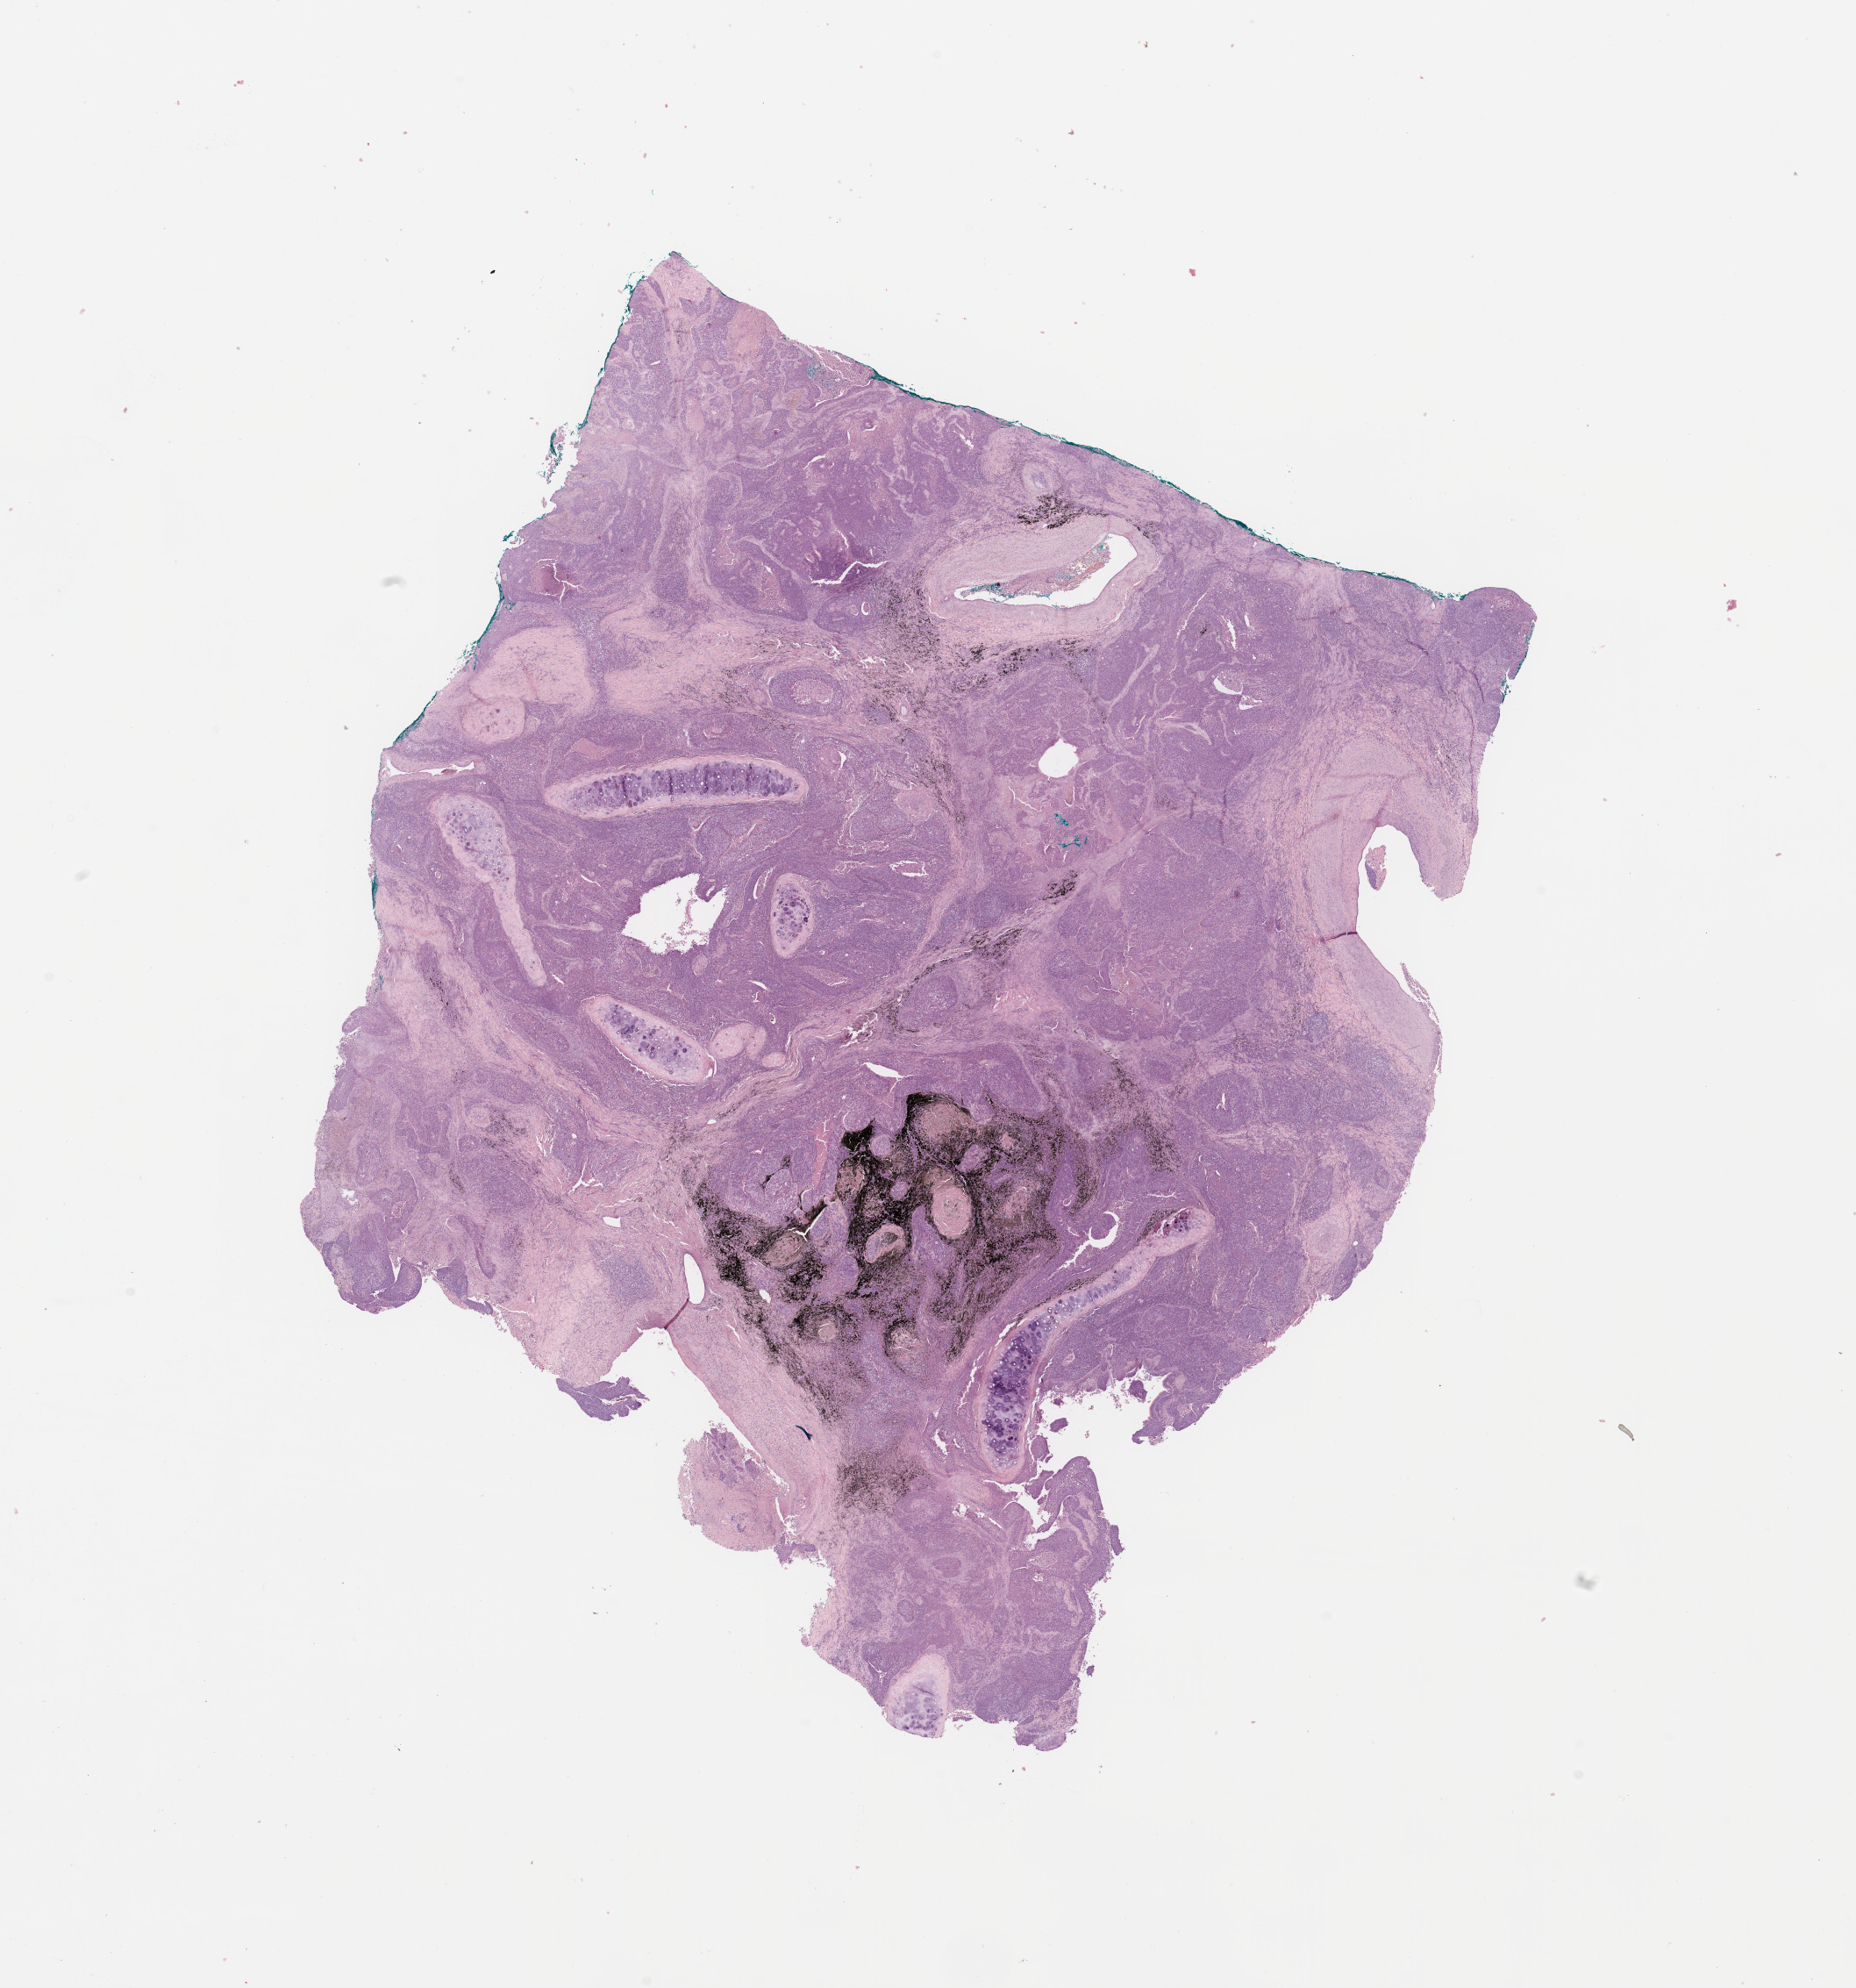
Whole-slide histology image, Hematoxylin and eosin (H&E) stained — a low-resolution overview of the entire scanned area, about 16.7 x 17.9 mm (slide scanned at 20x); lung, tumour tissue. Male, 75 y/o. Histologic grade: G2 (moderately differentiated).
• histologic diagnosis: Squamous cell carcinoma, NOS
• AJCC pathologic stage: IIIA
• primary tumour site (as recorded): right lower lobe